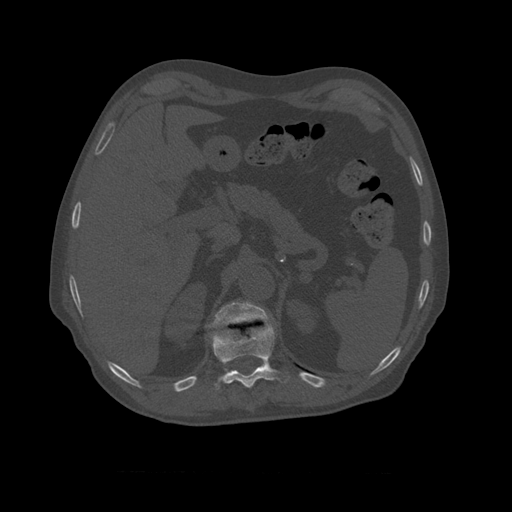
CT including the spine, one axial slice. Slice 398 of 450 in the series (ordered by position). Reconstruction kernel STANDARD. Bone window (W 1800 / L 400 HU). 512 × 512 image matrix, field of view 405 × 405 mm. Patient age 75 years. Case-level facts recorded for this patient, not image findings: primary cancer: prostate.
Annotated regions visible in this slice (semi-automatically segmented with operator editing):
- T10 vertebra: bounding box (x1, y1, x2, y2) in pixels: (210, 322, 290, 390)
- T11 vertebra: (209, 301, 273, 329)